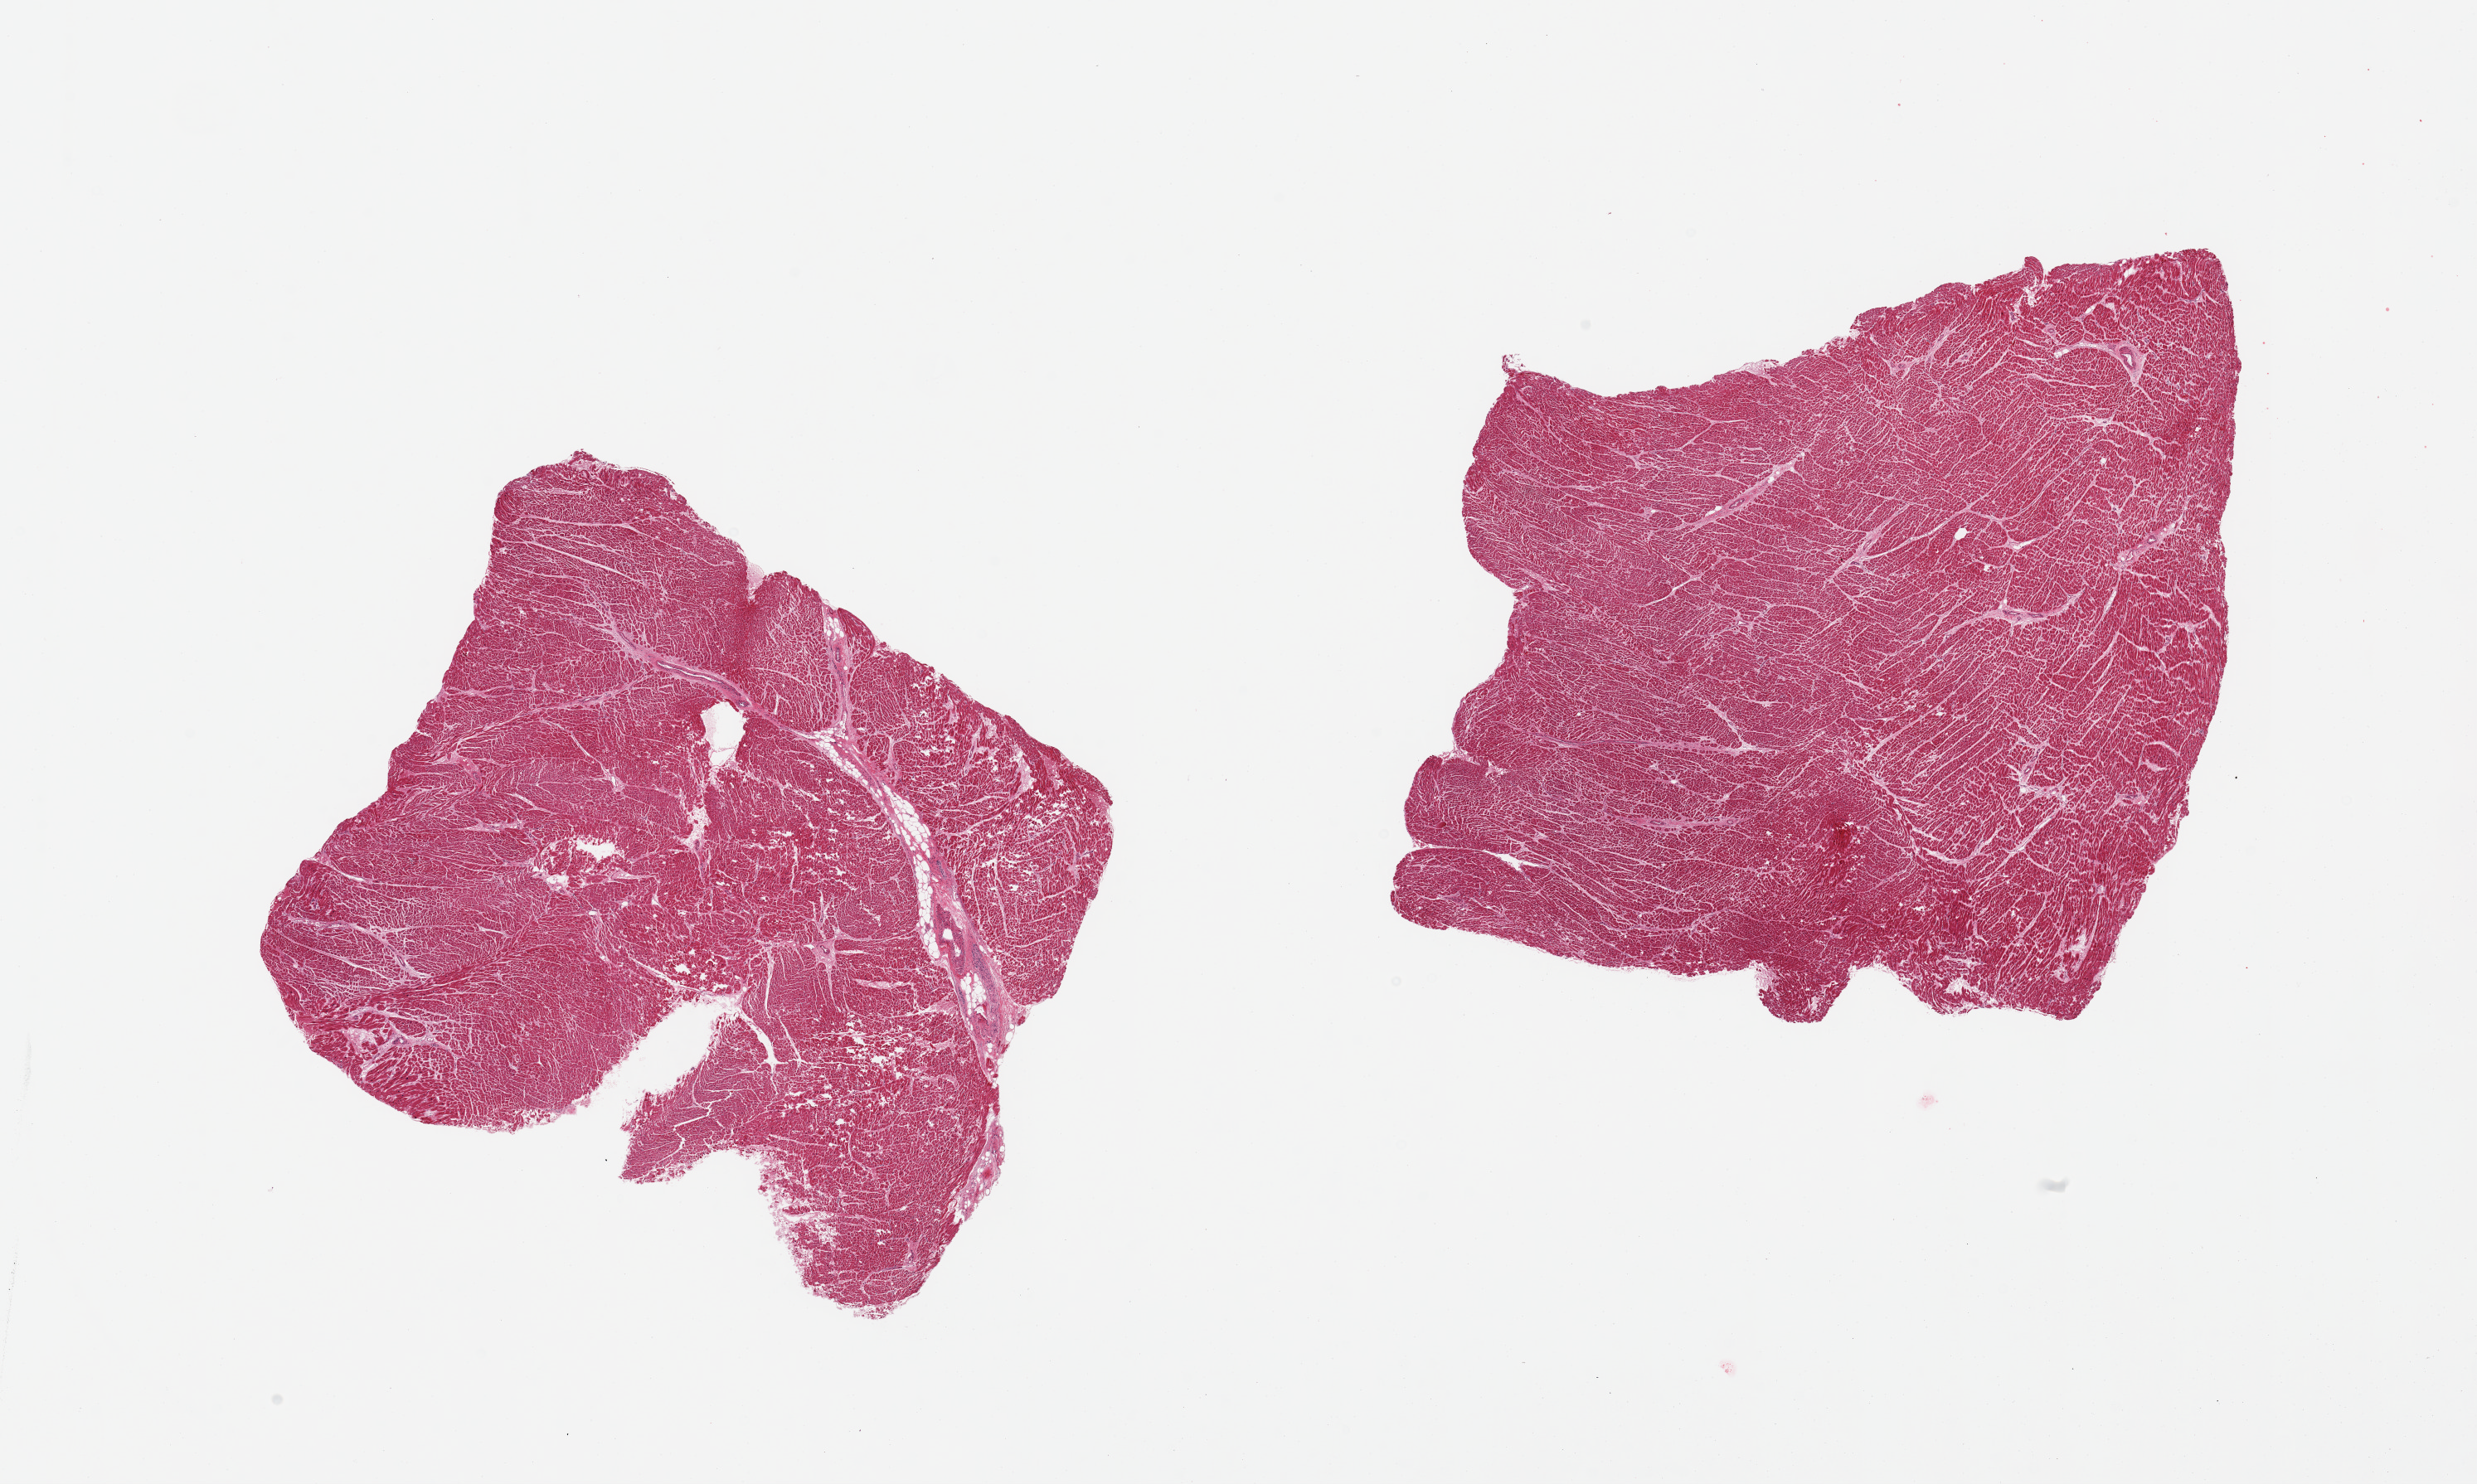
Digitized hematoxylin and eosin (H&E)-stained section, brightfield, shown as a low-resolution overview of the whole scanned area (about 23.6 x 14.2 mm, slide scanned at 20x), PAXgene-fixed, paraffin-embedded tissue, sampled site (target tissue): heart, donor tissue sample. Female donor.
* pathologist's review note for this sample: 2 pieces, minimal interstitial fibrosis